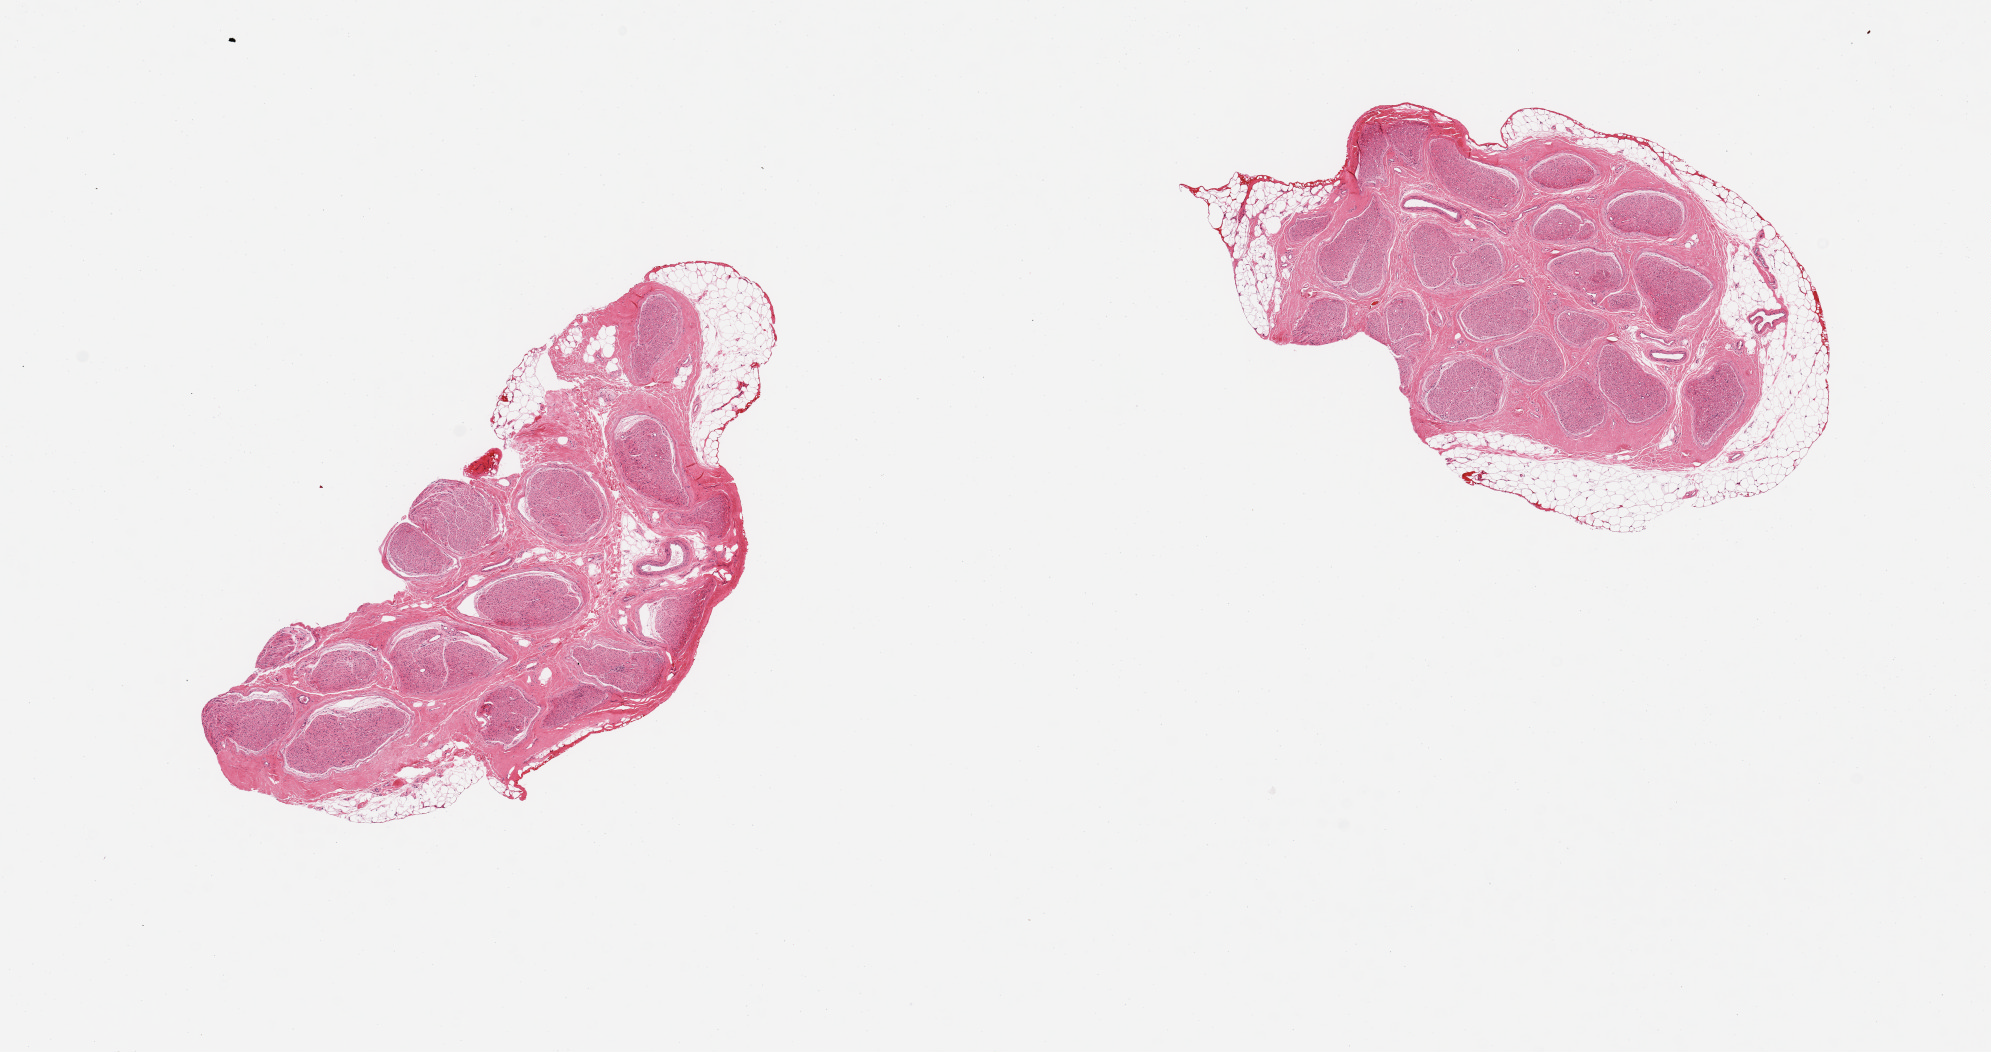
H&E whole-slide image, shown as a low-resolution overview of the whole scanned area (about 15.8 x 8.3 mm); PAXgene-fixed, paraffin-embedded tissue; target tissue: tibial nerve; donor tissue sample.
Review note (as recorded): 2 pieces; up to 0.5mm thick external fat on both.